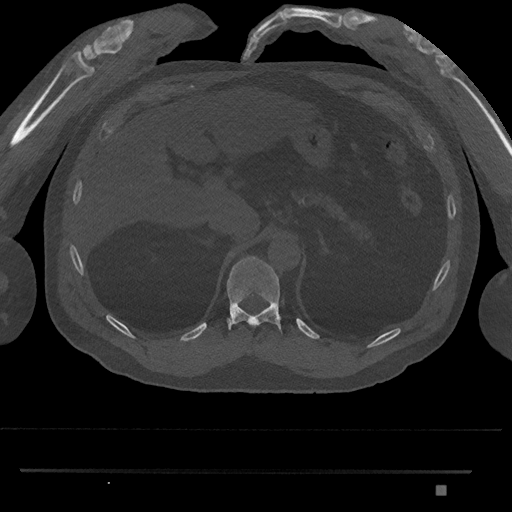
CT including the spine, one axial slice; 120 kVp; bone window (W 1800 / L 400 HU); 0.5 mm slice thickness; 512 × 512 image matrix, field of view 429 × 429 mm. Patient: male, 65 years. Case-level facts recorded for this patient, not image findings: primary cancer: prostate.
Annotated regions visible in this slice (semi-automatic segmentation, software-assisted and operator-edited):
- T11 vertebra: bounding box <226,256,281,330> (left, top, right, bottom; pixels)